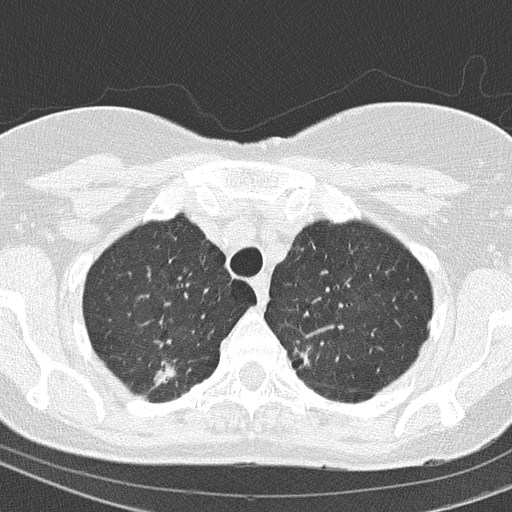
Low-dose screening chest CT, one axial slice. Slice 128 of 154 in the series (ordered by position). Lung window (W 1500 / L -600 HU). 2 mm slice thickness. 512 × 512 image matrix.
Structures marked on this image (expert manual segmentation):
- lesion 1 (tumor, upper lobe of right lung): bounding box (x1, y1, x2, y2) in pixels: (153, 361, 176, 388)